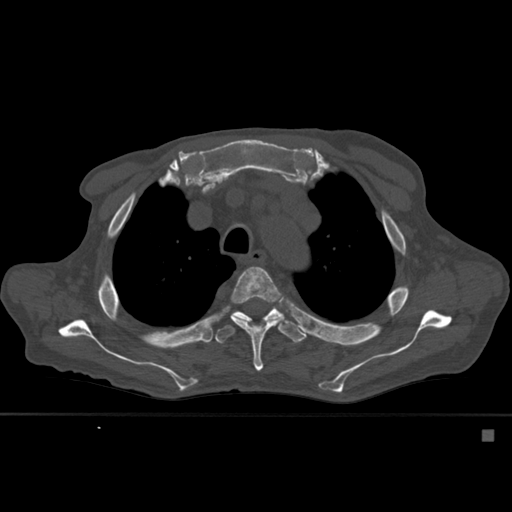
CT including the spine, one axial slice. Slice 412 of 527 in the series (ordered by position). Bone window (W 1800 / L 400 HU). 512 × 512 image matrix, field of view 373 × 373 mm. Male patient, age 78 years. Case-level facts recorded for this patient, not image findings: primary cancer: prostate.
Annotated regions visible in this slice (semi-automatic segmentation, software-assisted and operator-edited):
- T4 vertebra: bounding box [x1, y1, x2, y2] px = [230, 266, 287, 371]
- T5 vertebra: [215, 307, 308, 344]